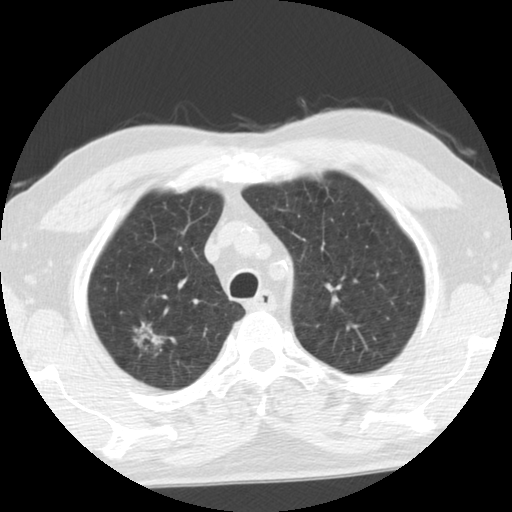
Low-dose screening chest CT, one axial slice; slice 91 of 116 in the series (ordered by position); reconstruction kernel STANDARD; 140 kVp; lung window (W 1500 / L -600 HU); 2.5 mm slice thickness; 512 × 512 image matrix, field of view 330 × 330 mm.
Outlined on this slice (manually delineated by an expert):
- lesion 1 (tumor, upper lobe of right lung): bounding box <133,320,171,356> (left, top, right, bottom; pixels)